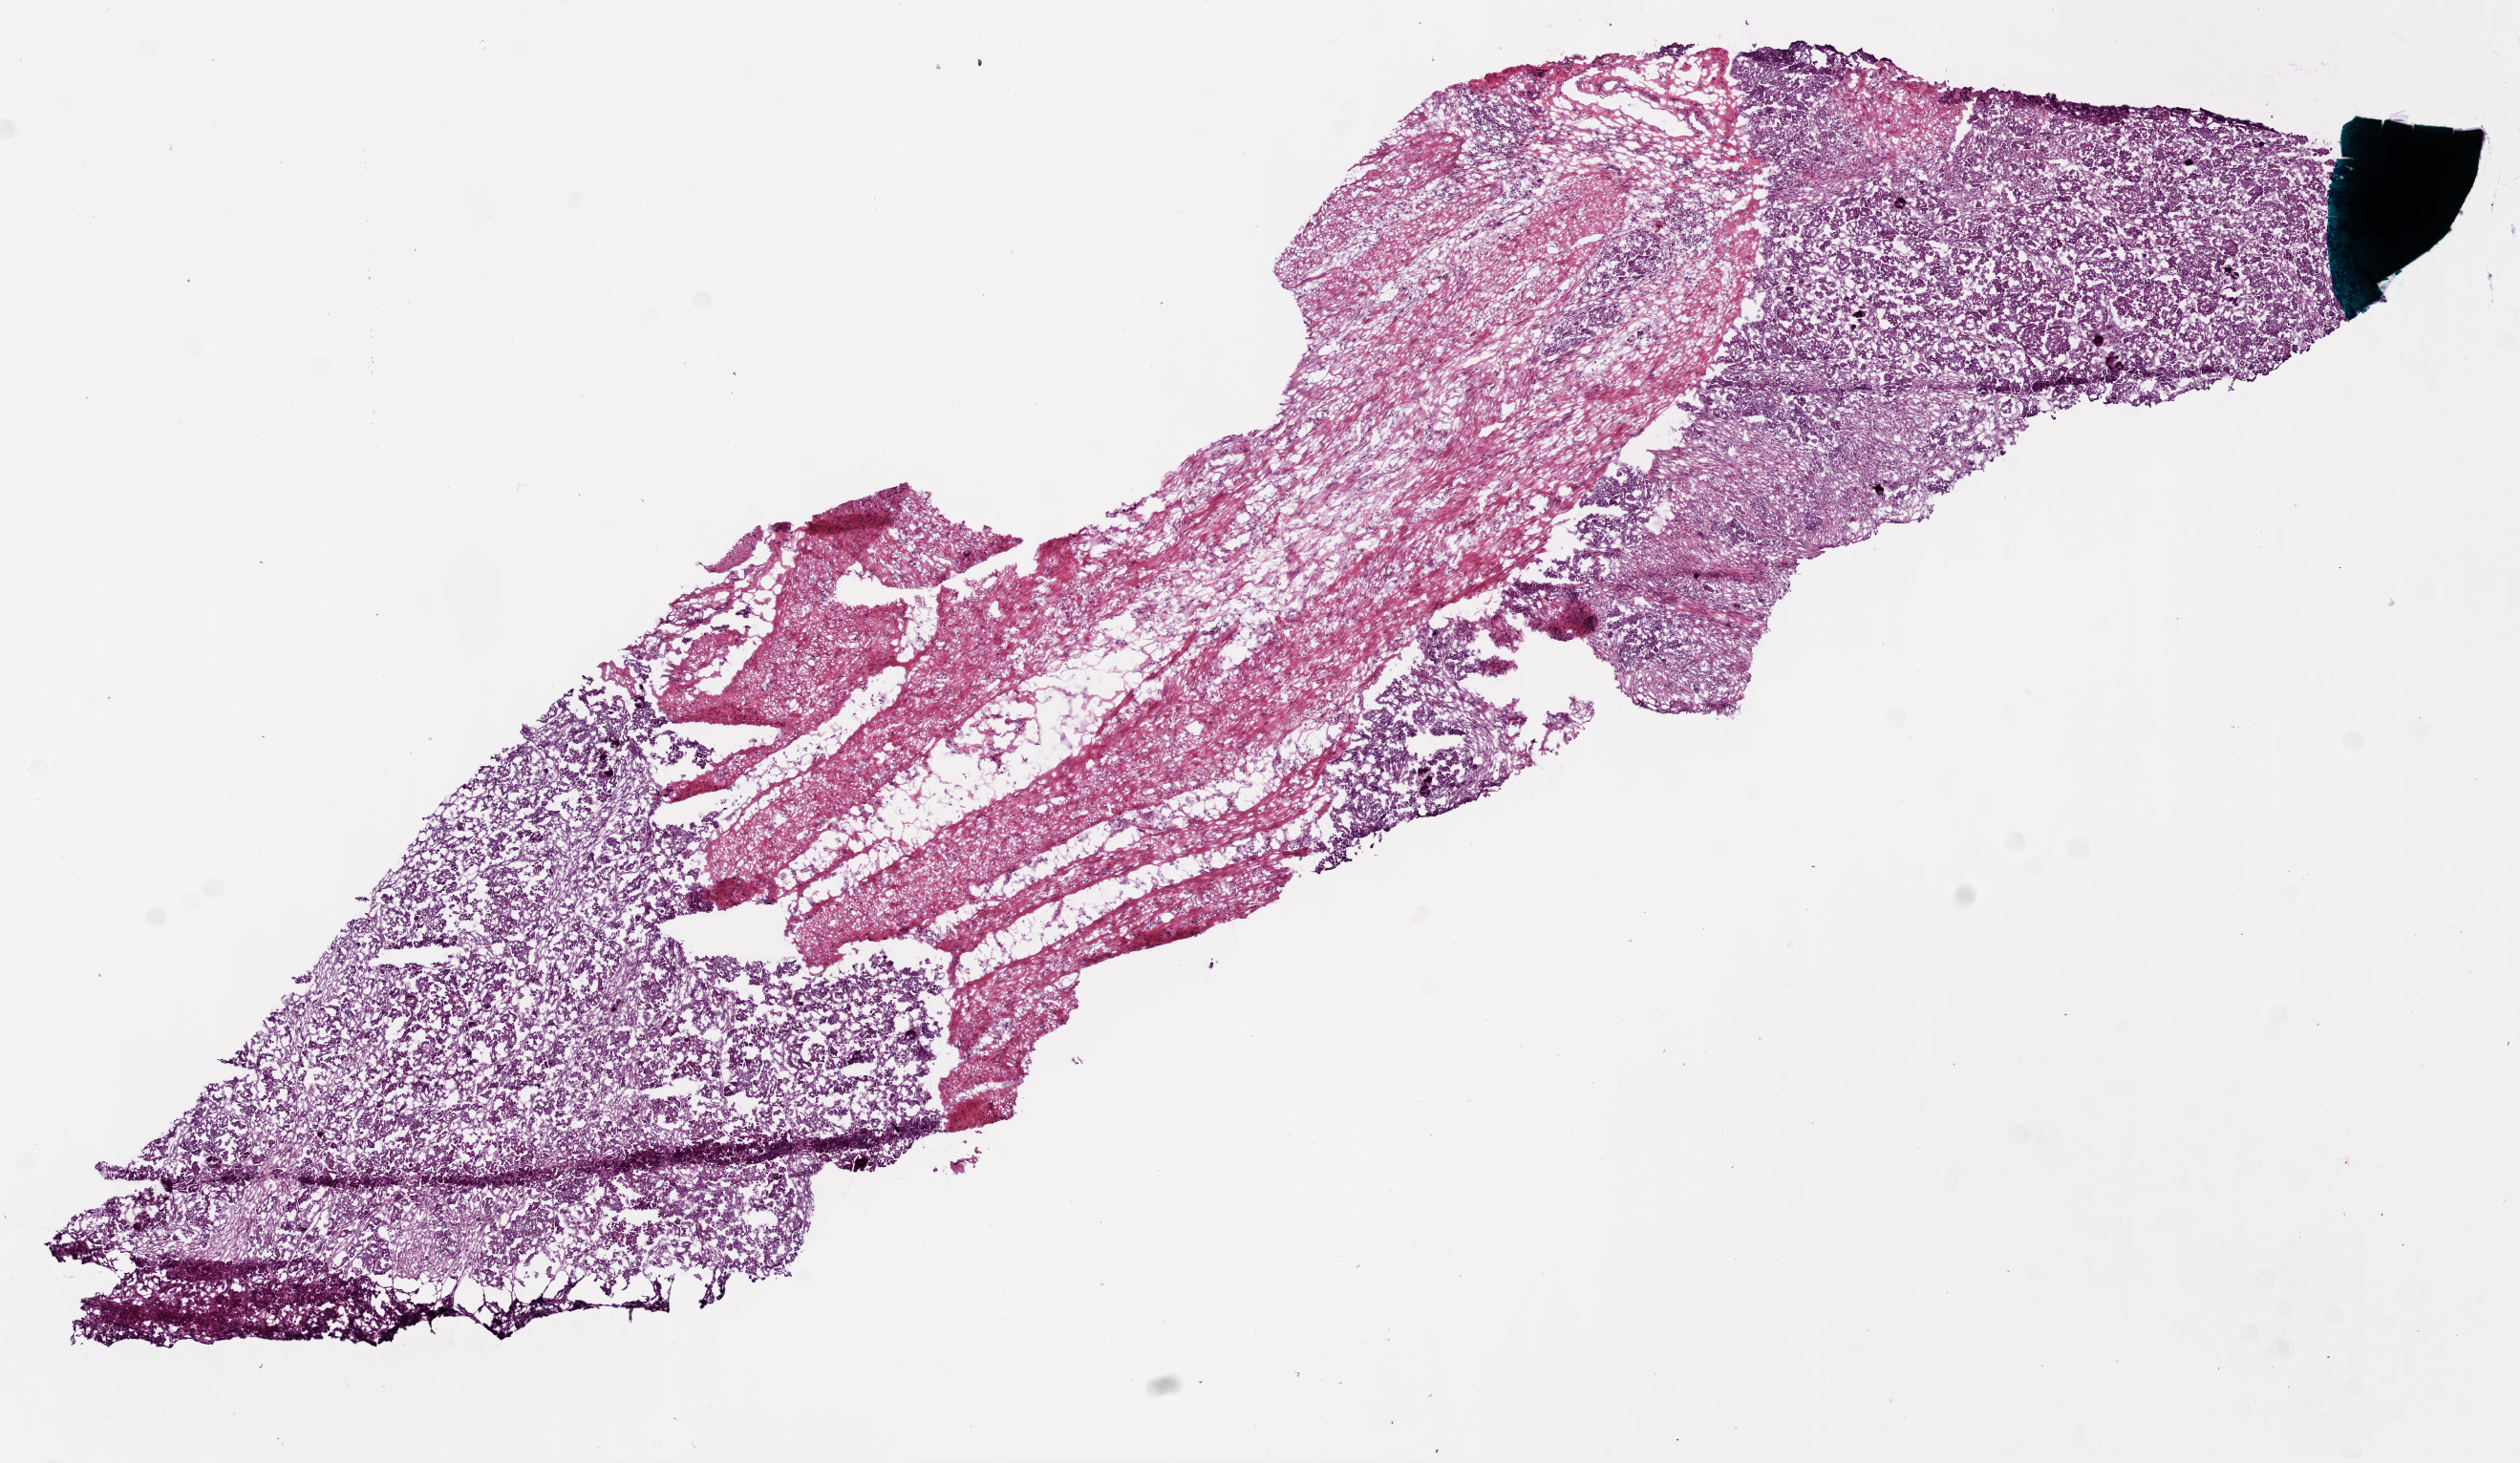
Whole-slide histology image, H&E-stained — whole scanned area (about 10.6 x 6.2 mm) shown as a low-resolution overview. Frozen section from the bottom of the tissue portion. Primary tumour sample from the ovary. Patient: female, age at initial diagnosis 78 years. Composition of this section per pathologist review: tumour cells 50%, tumour nuclei 84%.
Diagnosis: Serous cystadenocarcinoma, NOS.